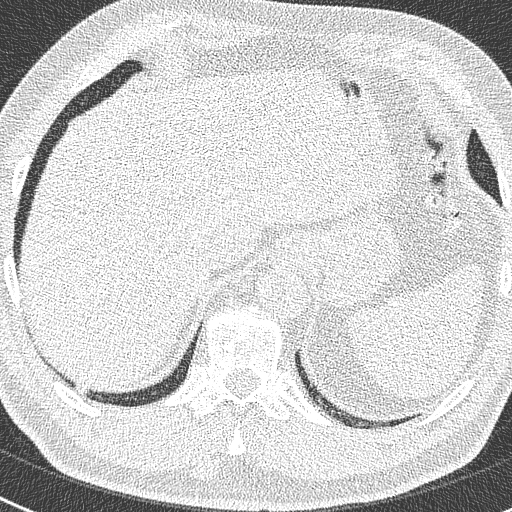
Chest CT (low-dose screening protocol), one axial image. Second annual screen. Lung window (W 1500 / L -600 HU). Lung (sharp) reconstruction kernel (B50f). Slice 240 of 299 in the series. 512 × 512 image matrix, field of view 300 × 300 mm. Male, age 63 years at enrolment. Former smoker at enrolment.
• Lesion marked by an expert reader, bounding box [x1, y1, x2, y2] px = [65, 376, 97, 404].
• No non-calcified nodule or mass ≥4 mm was recorded by the screening reader at this exam.
• Lung cancer was diagnosed 262 days after this screen: adenocarcinoma, NOS, right lower lobe, moderately differentiated (G2), stage IIIB (AJCC 6th edition), 17 mm at pathology.